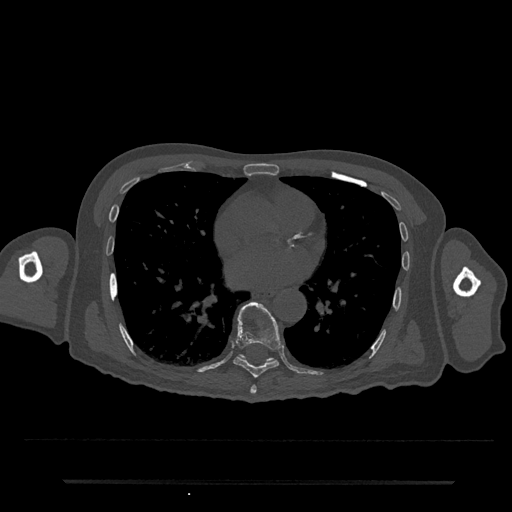
CT including the spine, one axial slice; position 413 of 797 along the scan axis; reconstruction kernel Br40s/3; bone window (W 1800 / L 400 HU); 0.5 mm slice thickness; 512 × 512 image matrix, field of view 427 × 427 mm. Patient: male, 74 years. Case-level facts recorded for this patient, not image findings: primary cancer: prostate.
Annotated regions visible in this slice (semi-automatically segmented with operator editing):
- T7 vertebra: box from (x=250, y=385) to (x=257, y=394) px
- T8 vertebra: (x=233, y=302)–(x=281, y=378)
- T9 vertebra: (x=239, y=354)–(x=274, y=362)